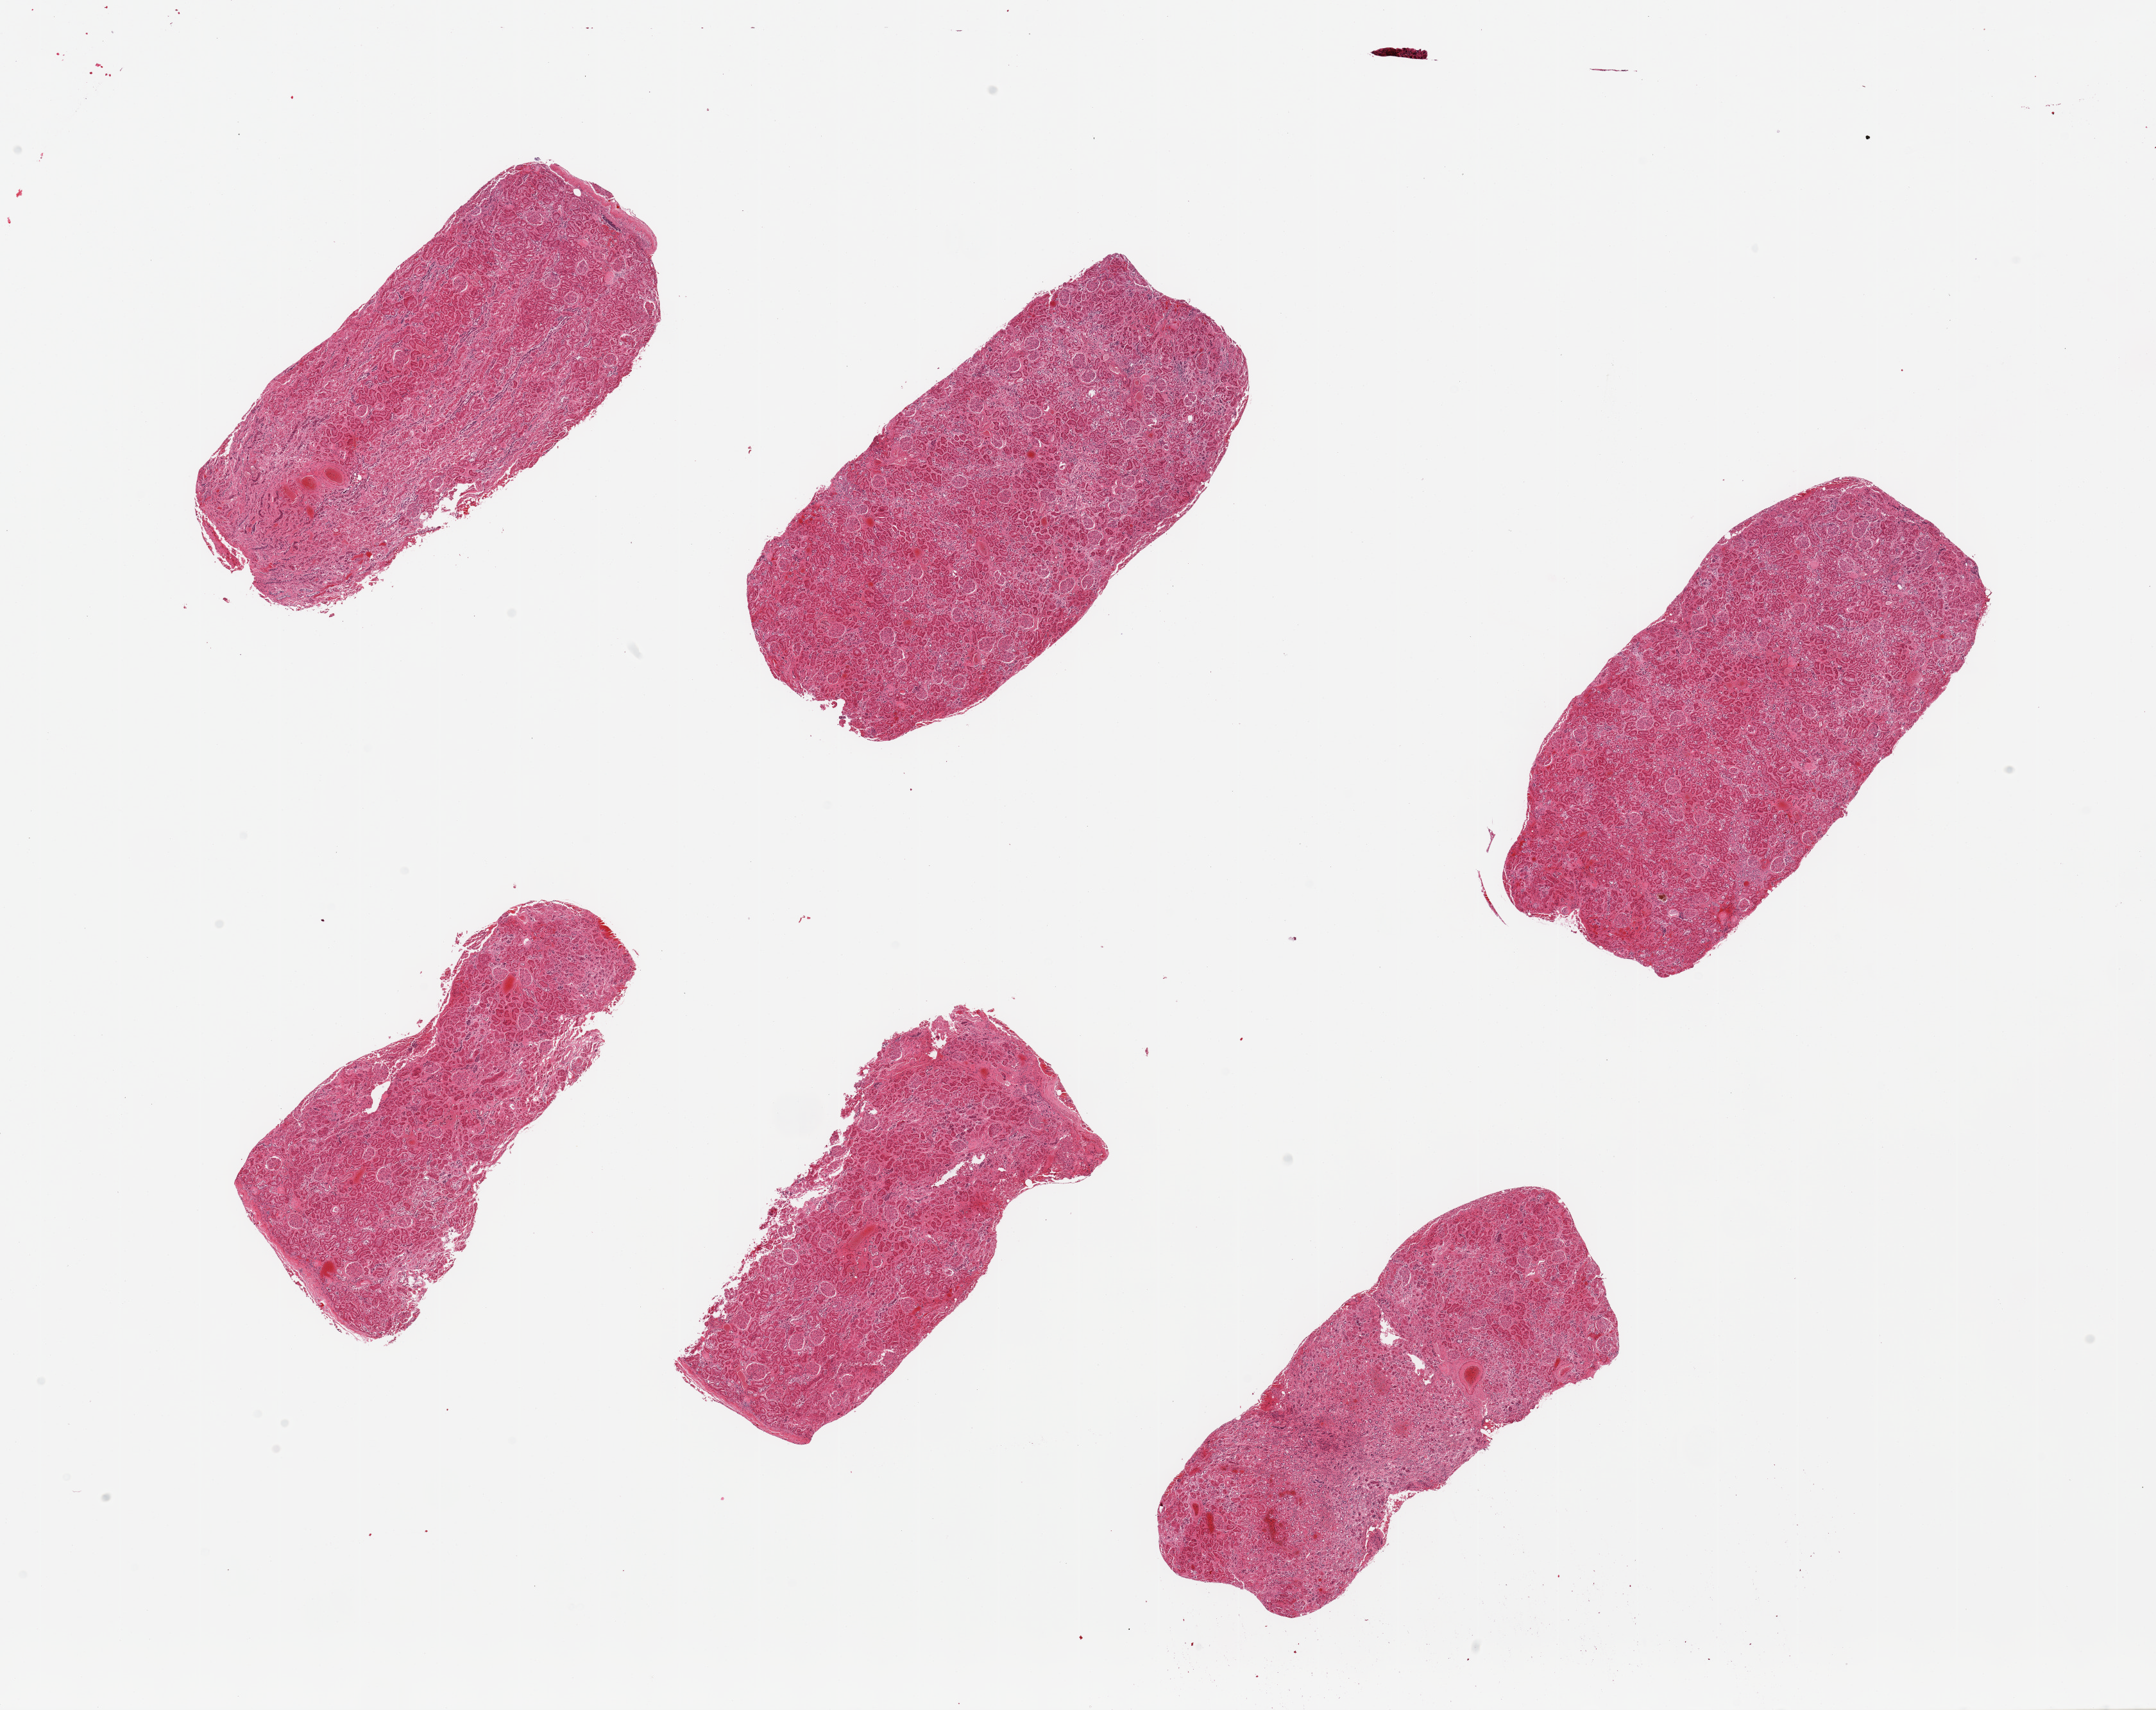
Haematoxylin and eosin whole-slide image — whole scanned area (about 26.6 x 21.1 mm) shown as a low-resolution overview. PAXgene-fixed paraffin-embedded (PFPE) section. Target tissue: renal cortex. Tissue donor sample.
Pathologist's review note for this sample: 6 pieces, glomeruli in all sections, few sclerotic.